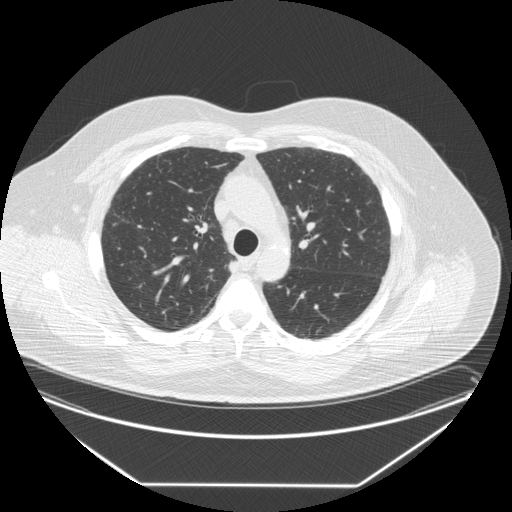
Low-dose screening chest CT, one axial slice. Slice 192 of 258 in the series (ordered by position). Reconstruction kernel STANDARD. Lung window (W 1500 / L -600 HU). 512 × 512 image matrix, field of view 440 × 440 mm.
Annotated regions visible in this slice (manually delineated by an expert):
- lesion 1 (tumor, upper lobe of right lung): box from (x=229, y=261) to (x=239, y=273) px